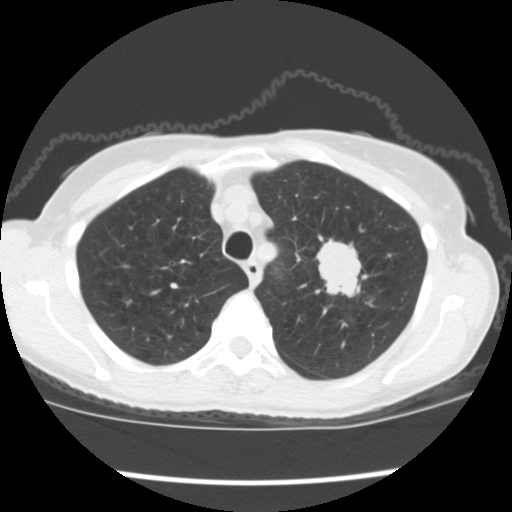
Chest CT (low-dose screening protocol), one axial image, baseline annual screen, lung window (W 1500 / L -600 HU), 2.5 mm slice thickness, slice 34 of 176 in the series, 512 × 512 image matrix. Female participant, aged 67 years at enrolment. Former smoker at enrolment.
Expert reader's lesion annotation, bounding box [x1, y1, x2, y2] px = [305, 235, 378, 311]. Screening reader's record for this exam (one nodule recorded; not confirmed to be the boxed lesion): non-calcified nodule or mass ≥4 mm, left upper lobe, 34 × 32 mm, spiculated (stellate) margins, soft tissue attenuation, pre-existing on the prior screen: no. Official screen result: positive, change unspecified: nodule(s) >= 4 mm or enlarging nodule(s), mass(es), or other non-specific abnormalities suspicious for lung cancer. Later outcome: lung cancer diagnosed 17 days after this screen — small cell carcinoma, NOS, left upper lobe, stage IIIA (AJCC 6th edition), 40 mm at pathology.